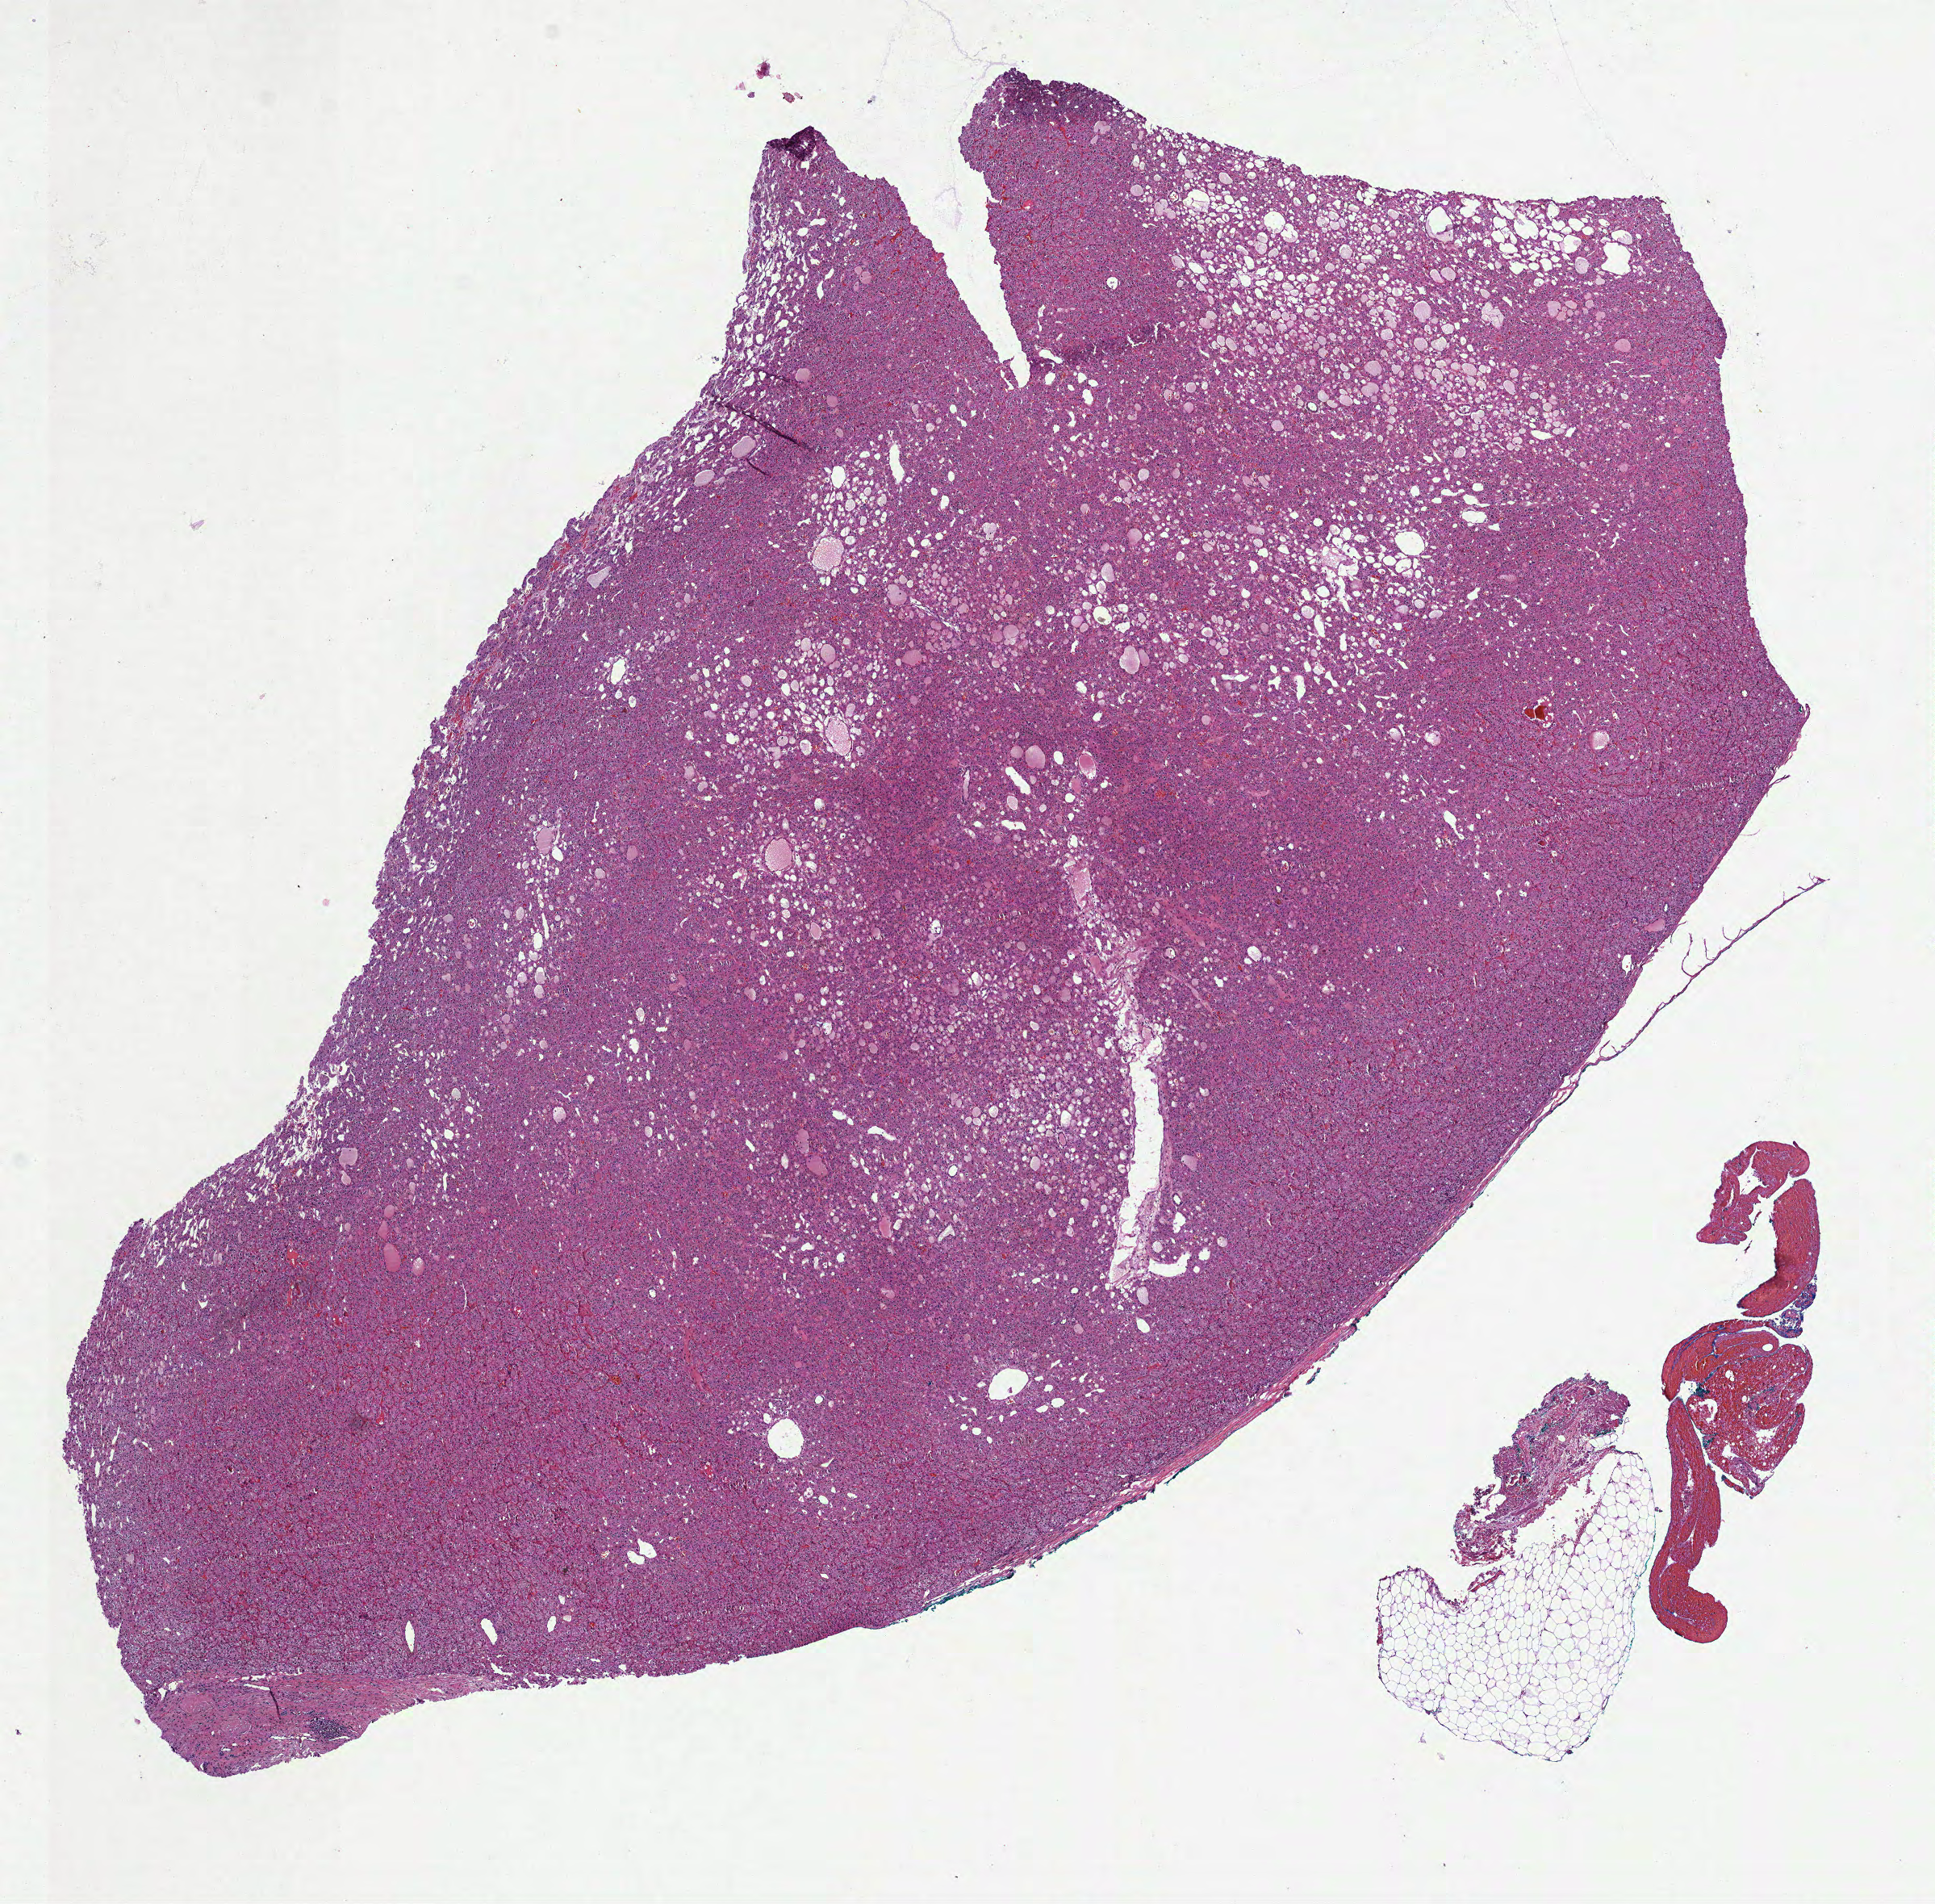
Digitized H&E-stained tissue section (whole slide) — shown as a low-resolution overview of the whole scanned area (about 9.7 x 9.5 mm, from a 40x scan); FFPE section; kidney, primary tumour sample. Female, age 75 years at initial diagnosis.
* laterality: left
* pathologic diagnosis: Renal cell carcinoma, chromophobe type
* AJCC pathologic stage: I